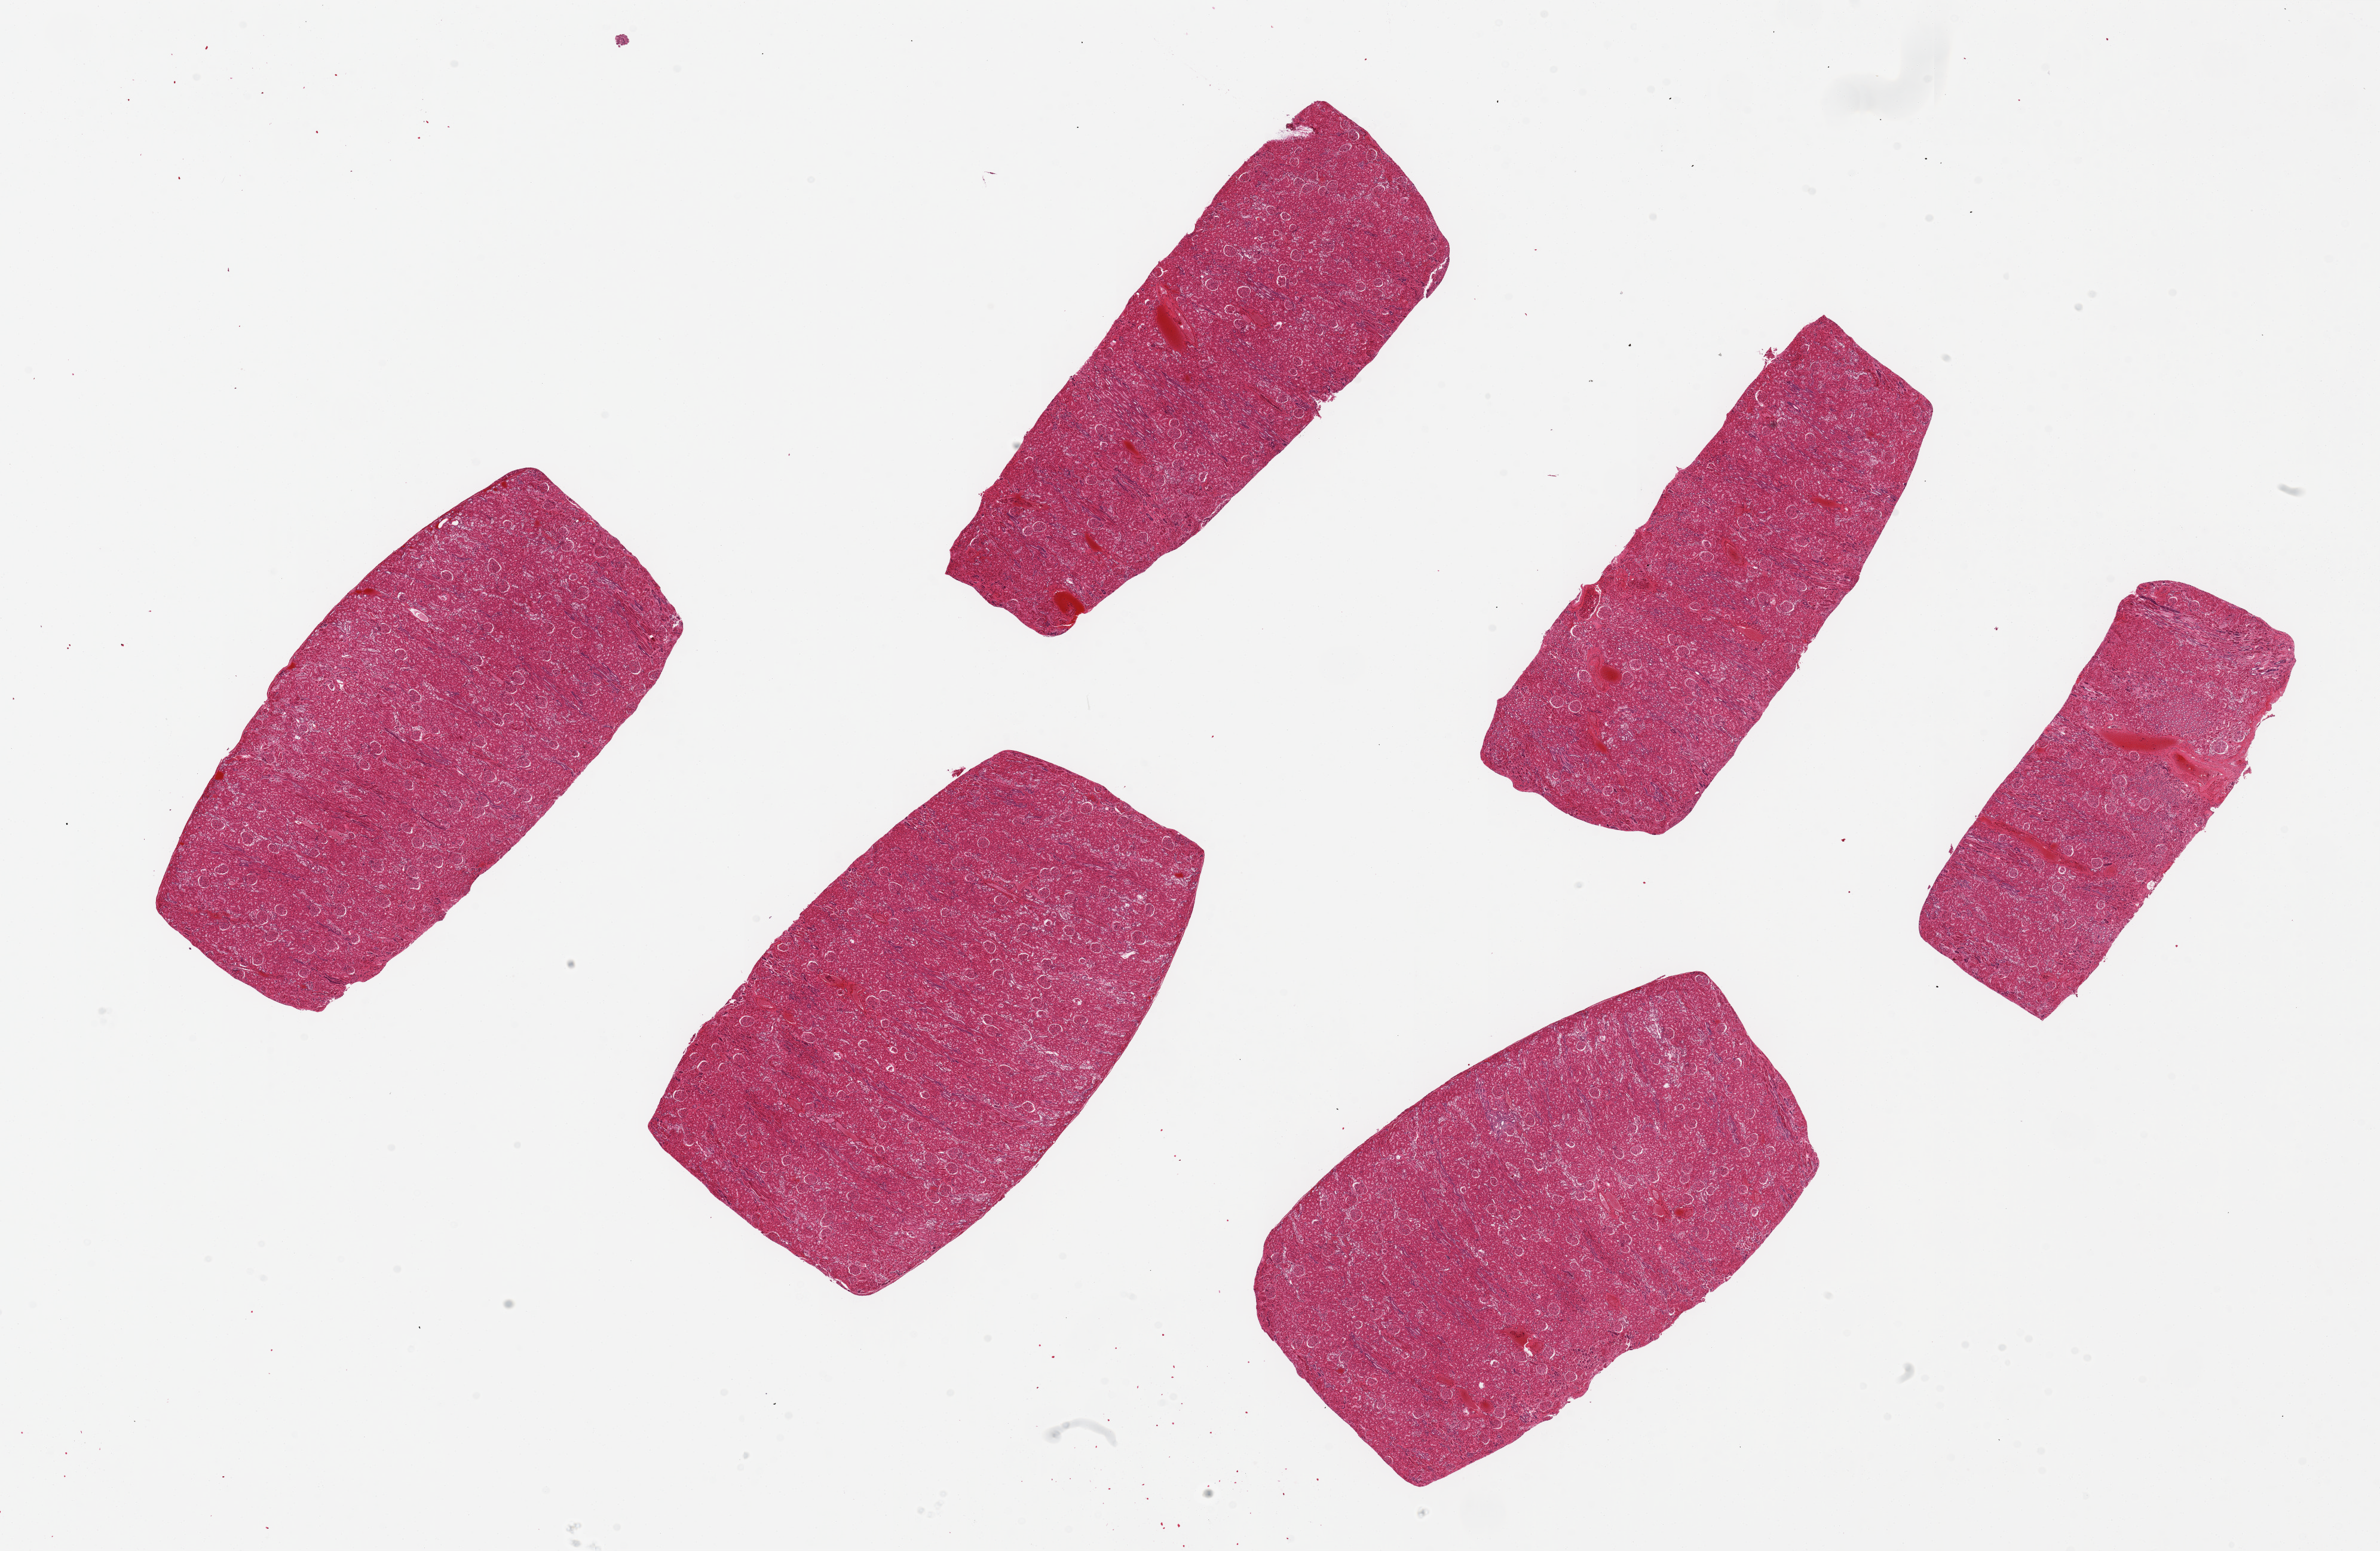
Digitized hematoxylin and eosin (H&E)-stained section, brightfield — a low-resolution overview of the entire scanned area, about 31.5 x 20.5 mm; PAXgene-fixed, paraffin-embedded tissue; target tissue: renal cortex; tissue donor sample. Male donor.
• pathologist's review note for this sample: 6 pieces up to 7.7x4.4 mm; good morphology; no lesions; moderate venous congestion